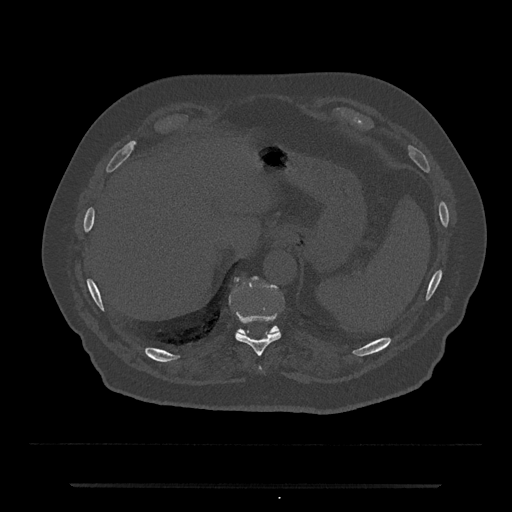
CT including the spine, one axial slice; position 691 of 797 along the scan axis; reconstruction kernel Br40s/3; 120 kVp; bone window (W 1800 / L 400 HU); 0.5 mm slice thickness; 512 × 512 image matrix, field of view 434 × 434 mm. Male patient, age 80 years. Case-level facts recorded for this patient, not image findings: primary cancer: prostate; vertebrae with lytic lesions (as recorded): L1, T11.
Structures marked on this image (semi-automatically segmented with operator editing):
- T10 vertebra: bounding box (x1, y1, x2, y2) in pixels: (235, 278, 281, 356)
- T11 vertebra: (237, 277, 280, 334)